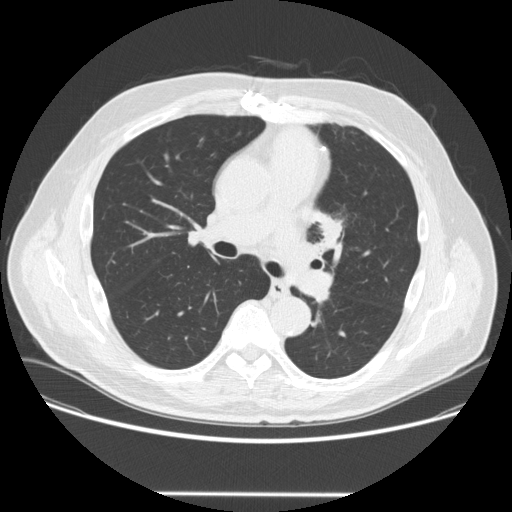
Chest CT (low-dose screening protocol), one axial image; third screening round (two years after baseline); lung window (W 1500 / L -600 HU); standard (soft-tissue) reconstruction kernel (STANDARD); 120 kVp; slice 97 of 253 in the series. Male, age 66 years at enrolment. Former smoker at enrolment.
- Expert-annotated lung lesion, bounding box (x1, y1, x2, y2) in pixels: (303, 208, 355, 255).
- The screening reader recorded 2 non-calcified nodules or masses ≥4 mm on this exam (left upper lobe, right lower lobe); which of them this box marks is not recorded.
- Official screen result: positive, other.
- Lung cancer was diagnosed 85 days after this screen: squamous cell carcinoma, NOS, left upper lobe, poorly differentiated (G3), stage IA (AJCC 6th edition), 27 mm at pathology.